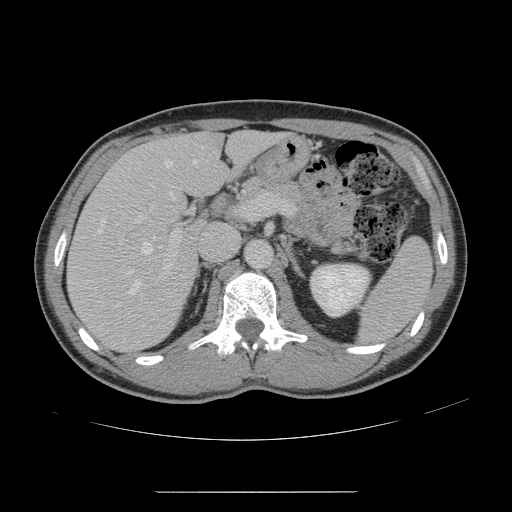
Contrast-enhanced abdominal CT, one axial slice. Slice 86 of 178 in the series (ordered by position). 120 kVp. Intravenous contrast given. Soft-tissue window (W 400 / L 40 HU). 512 × 512 image matrix. Male patient, age 53 years. Case-level facts recorded for this patient, not image findings: diagnosis: colorectal cancer liver metastases, imaged before liver resection; multiple liver metastases: yes; largest metastasis: 2.4 cm; disease in both lobes: no.
Outlined on this slice (outlined manually by an expert reader):
- hepatic veins: bounding box (x1, y1, x2, y2) in pixels: (97, 160, 196, 307)
- liver: (68, 133, 277, 351)
- planned liver remnant (the part of the liver to remain after resection): (152, 132, 278, 195)
- portal vein (with intrahepatic branches): (133, 193, 267, 280)